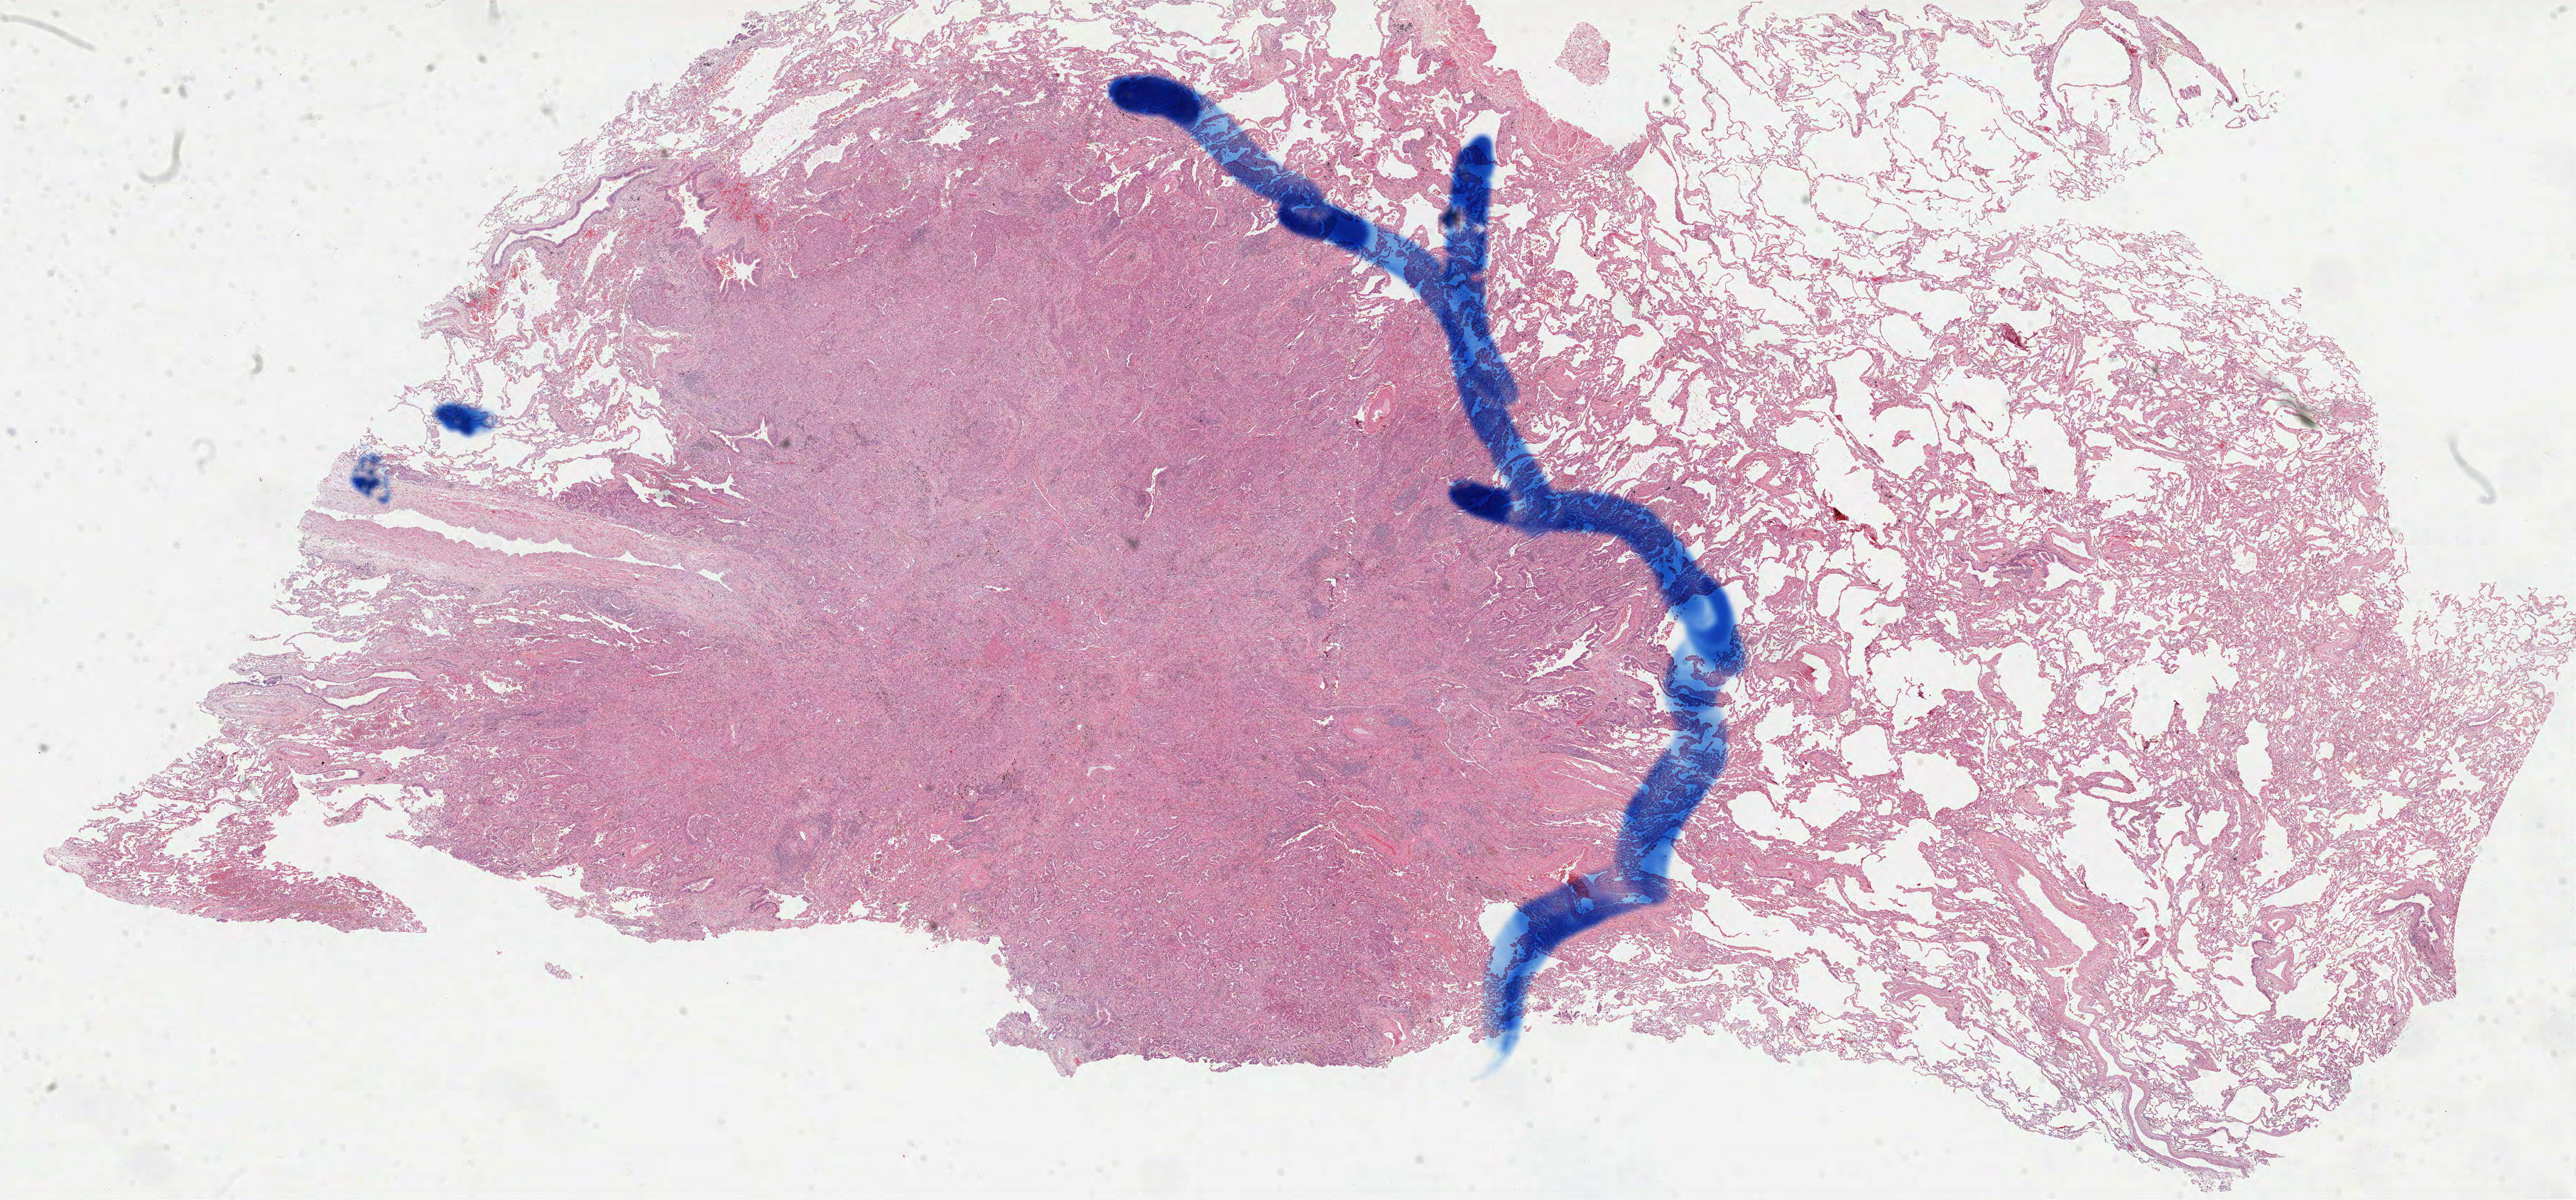
Whole-slide histology image, Hematoxylin and eosin (H&E) stained, a low-resolution overview of the entire scanned area, about 29.2 x 13.6 mm (from a 40x scan). Formalin-fixed paraffin-embedded (FFPE) diagnostic section. Lung, primary tumour sample. Female, age 49 years at initial diagnosis.
AJCC pathologic stage: IIIA (6th edition). Laterality: right. Diagnosis: Adenocarcinoma with mixed subtypes (upper lobe, lung).